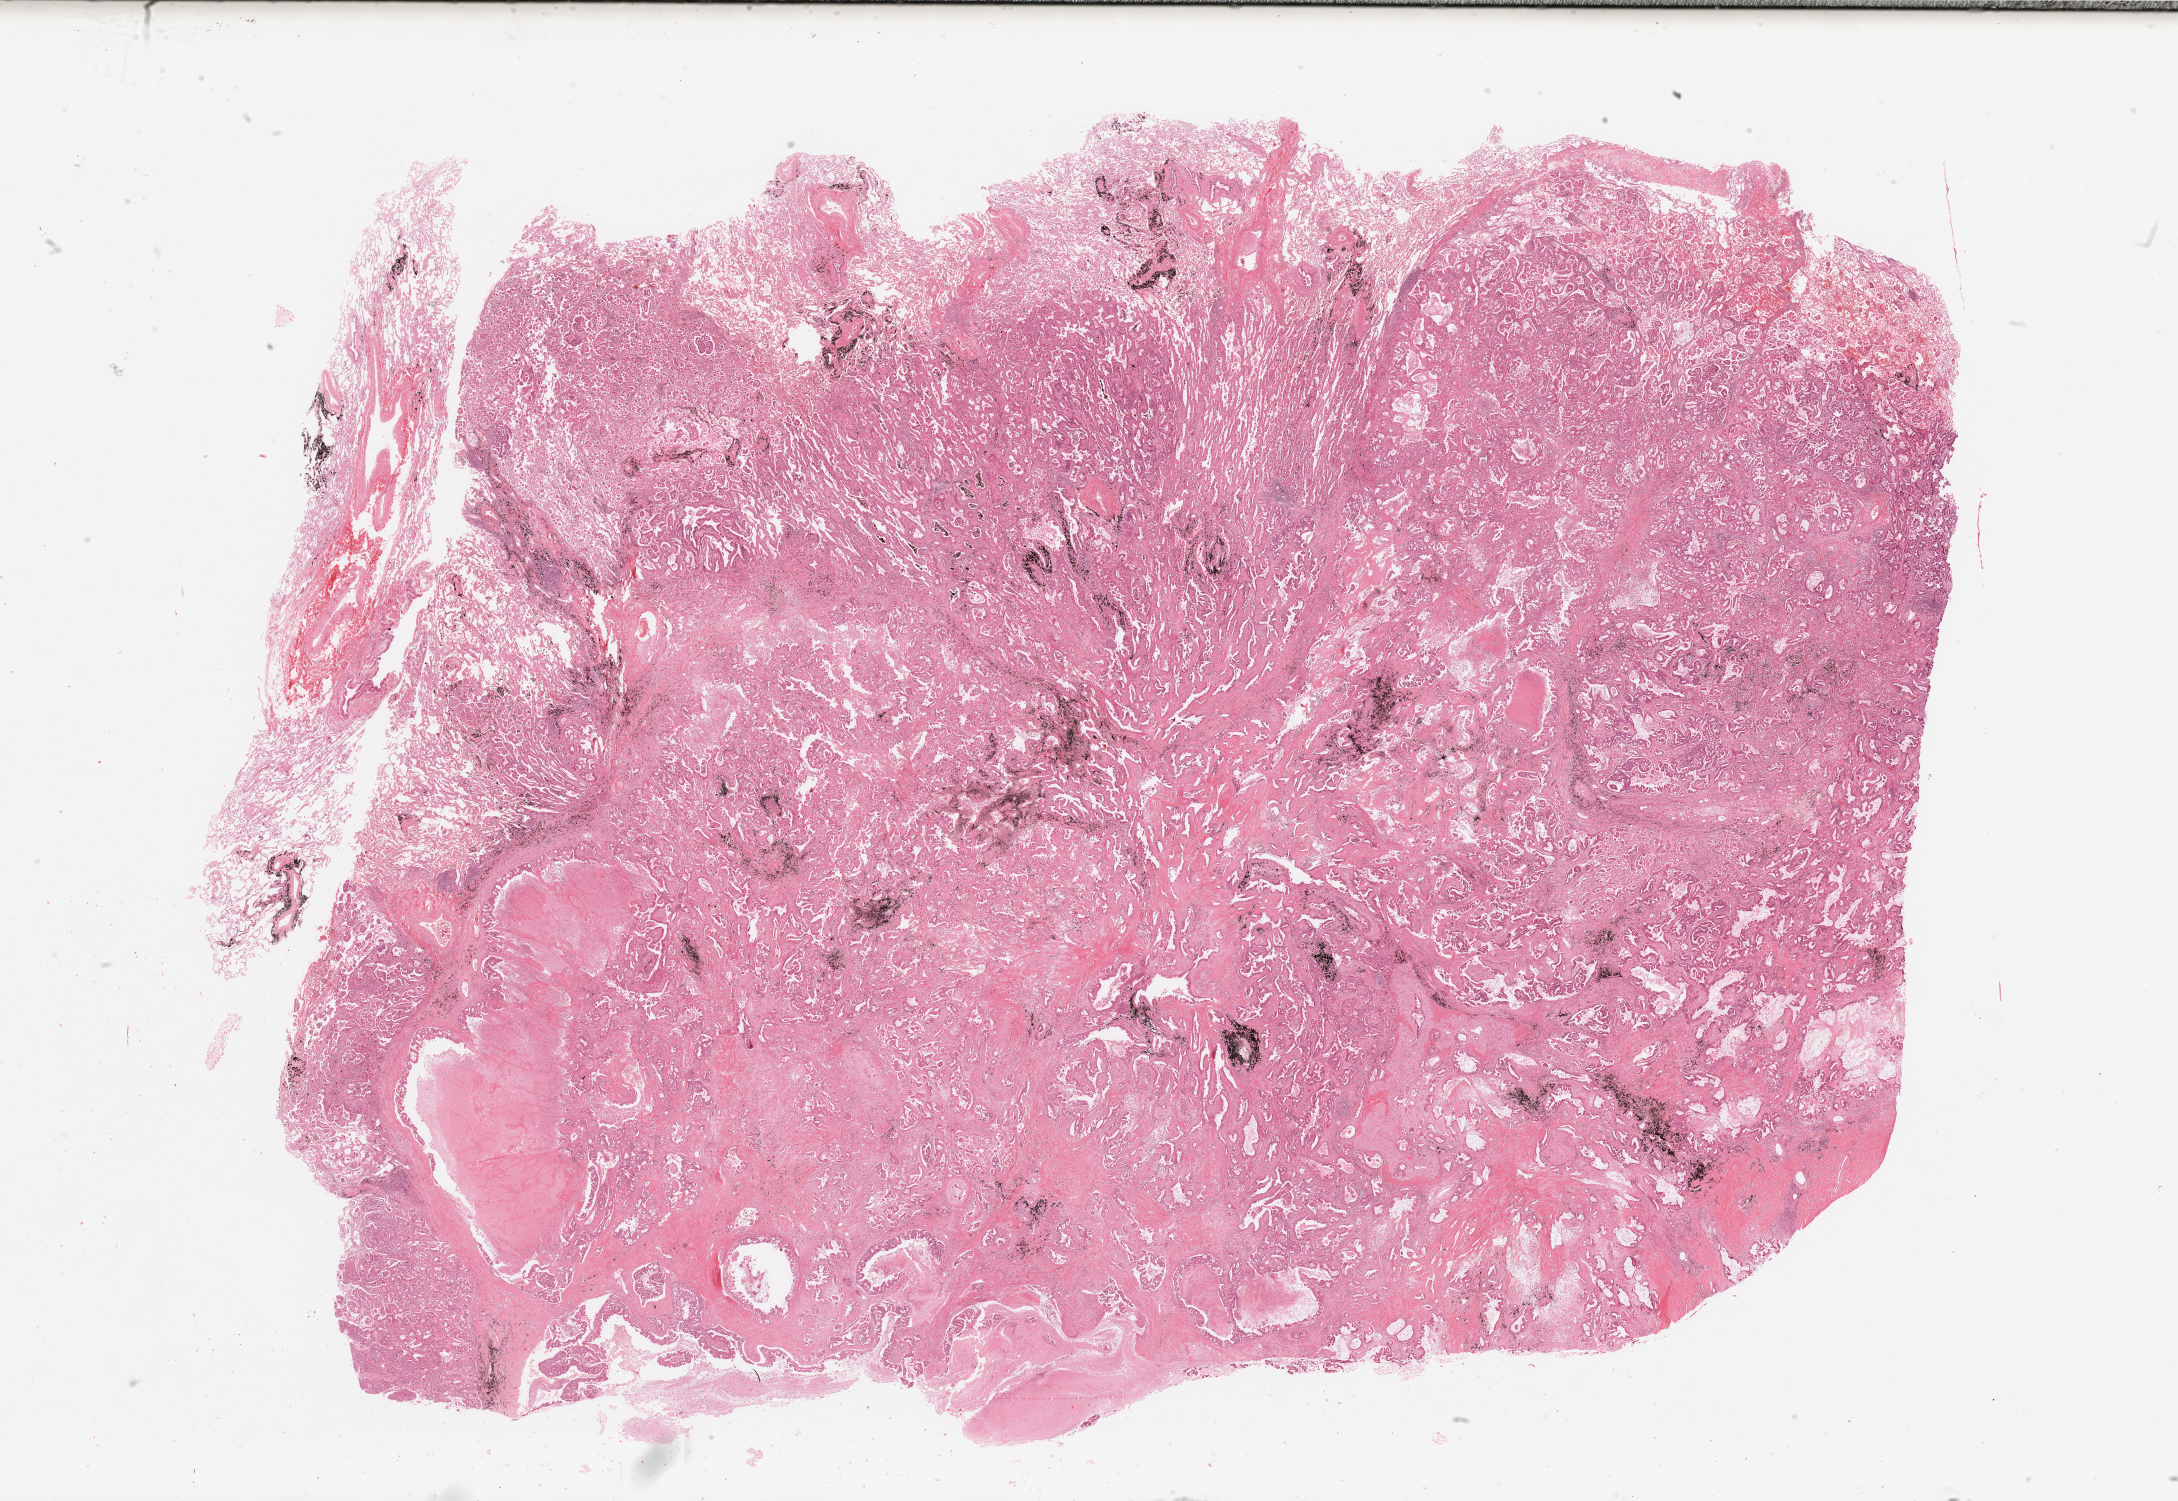
Digitized H&E tissue section (whole slide), shown as a low-resolution overview of the whole scanned area (about 34.5 x 23.7 mm); lung, tumour tissue. Male, 63 y/o.
Histologic diagnosis: Adenocarcinoma, NOS.